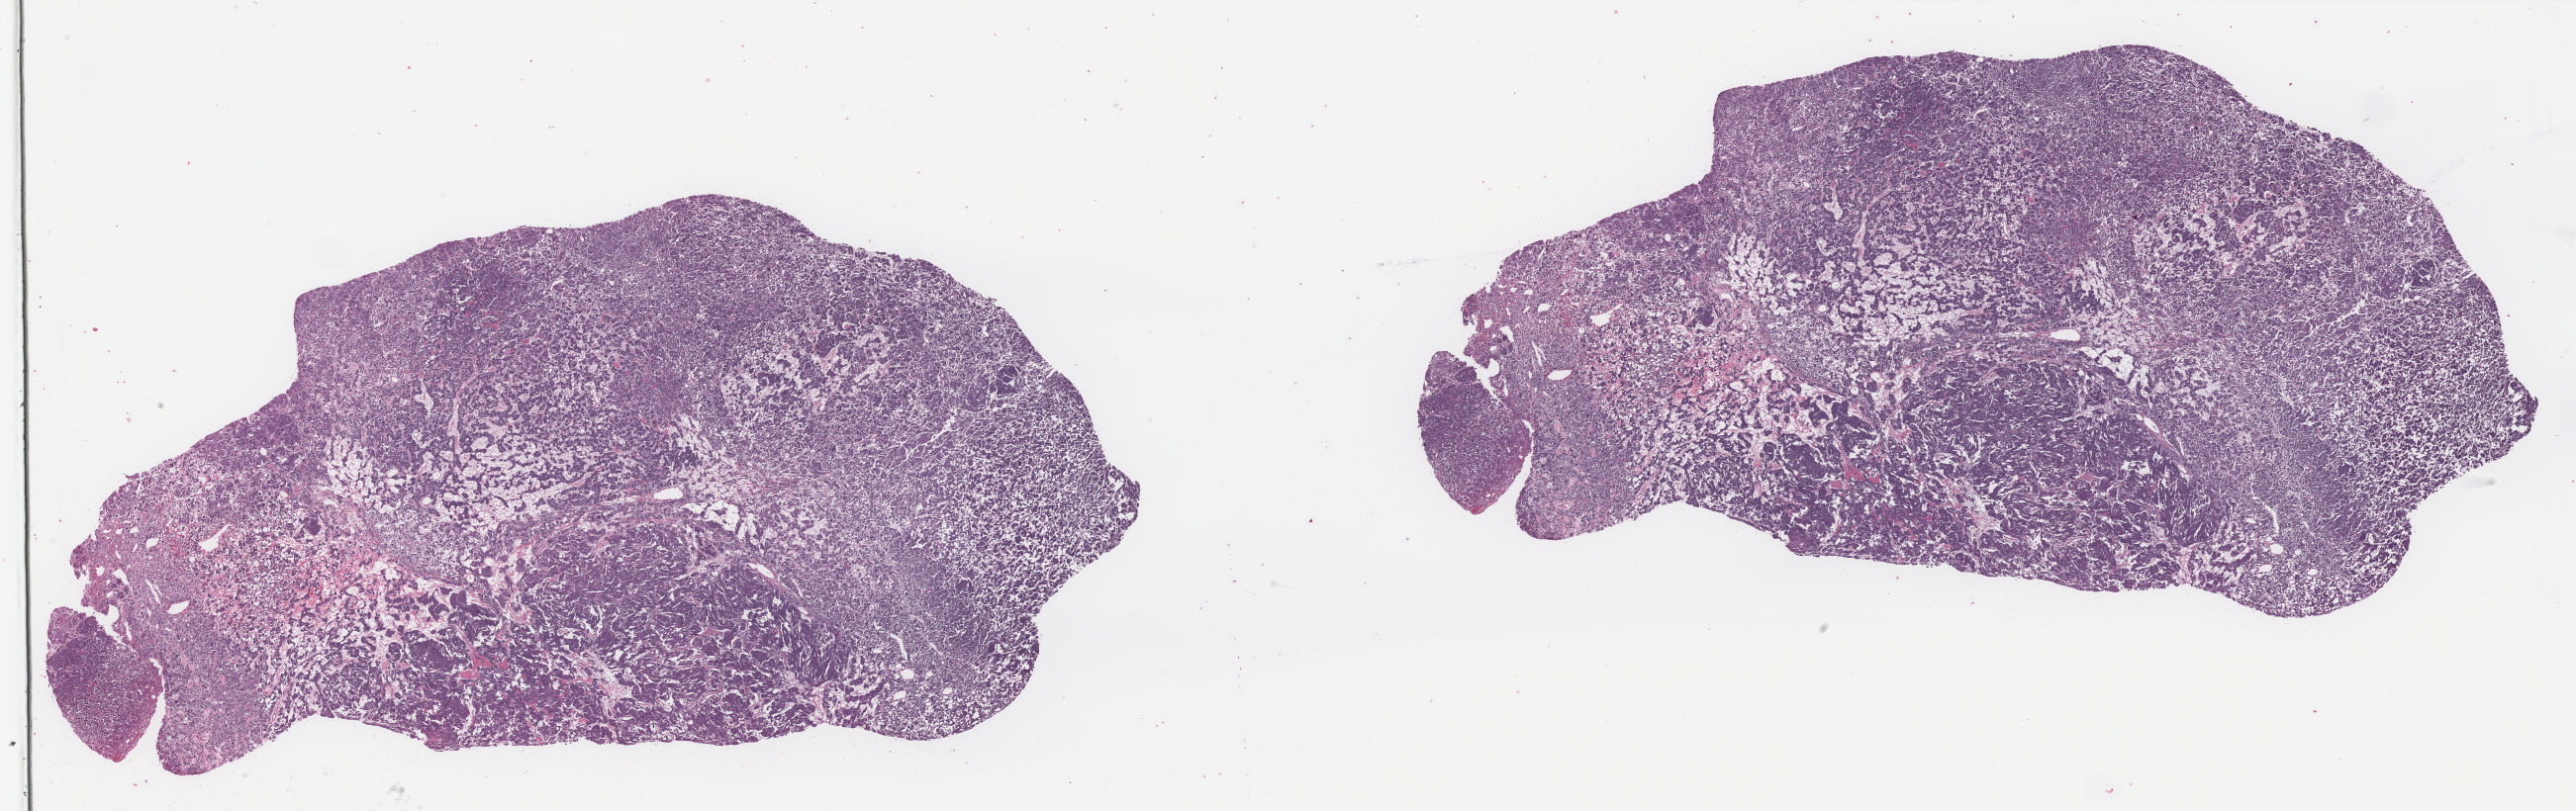
H&E whole-slide image — a low-resolution overview of the entire scanned area, about 41.2 x 13.0 mm (acquisition: 40x scan). FFPE section. Sample: primary tumour, adrenal gland. Patient: female, age at initial diagnosis 63 years.
• laterality: left
• pathologic diagnosis: Pheochromocytoma, malignant